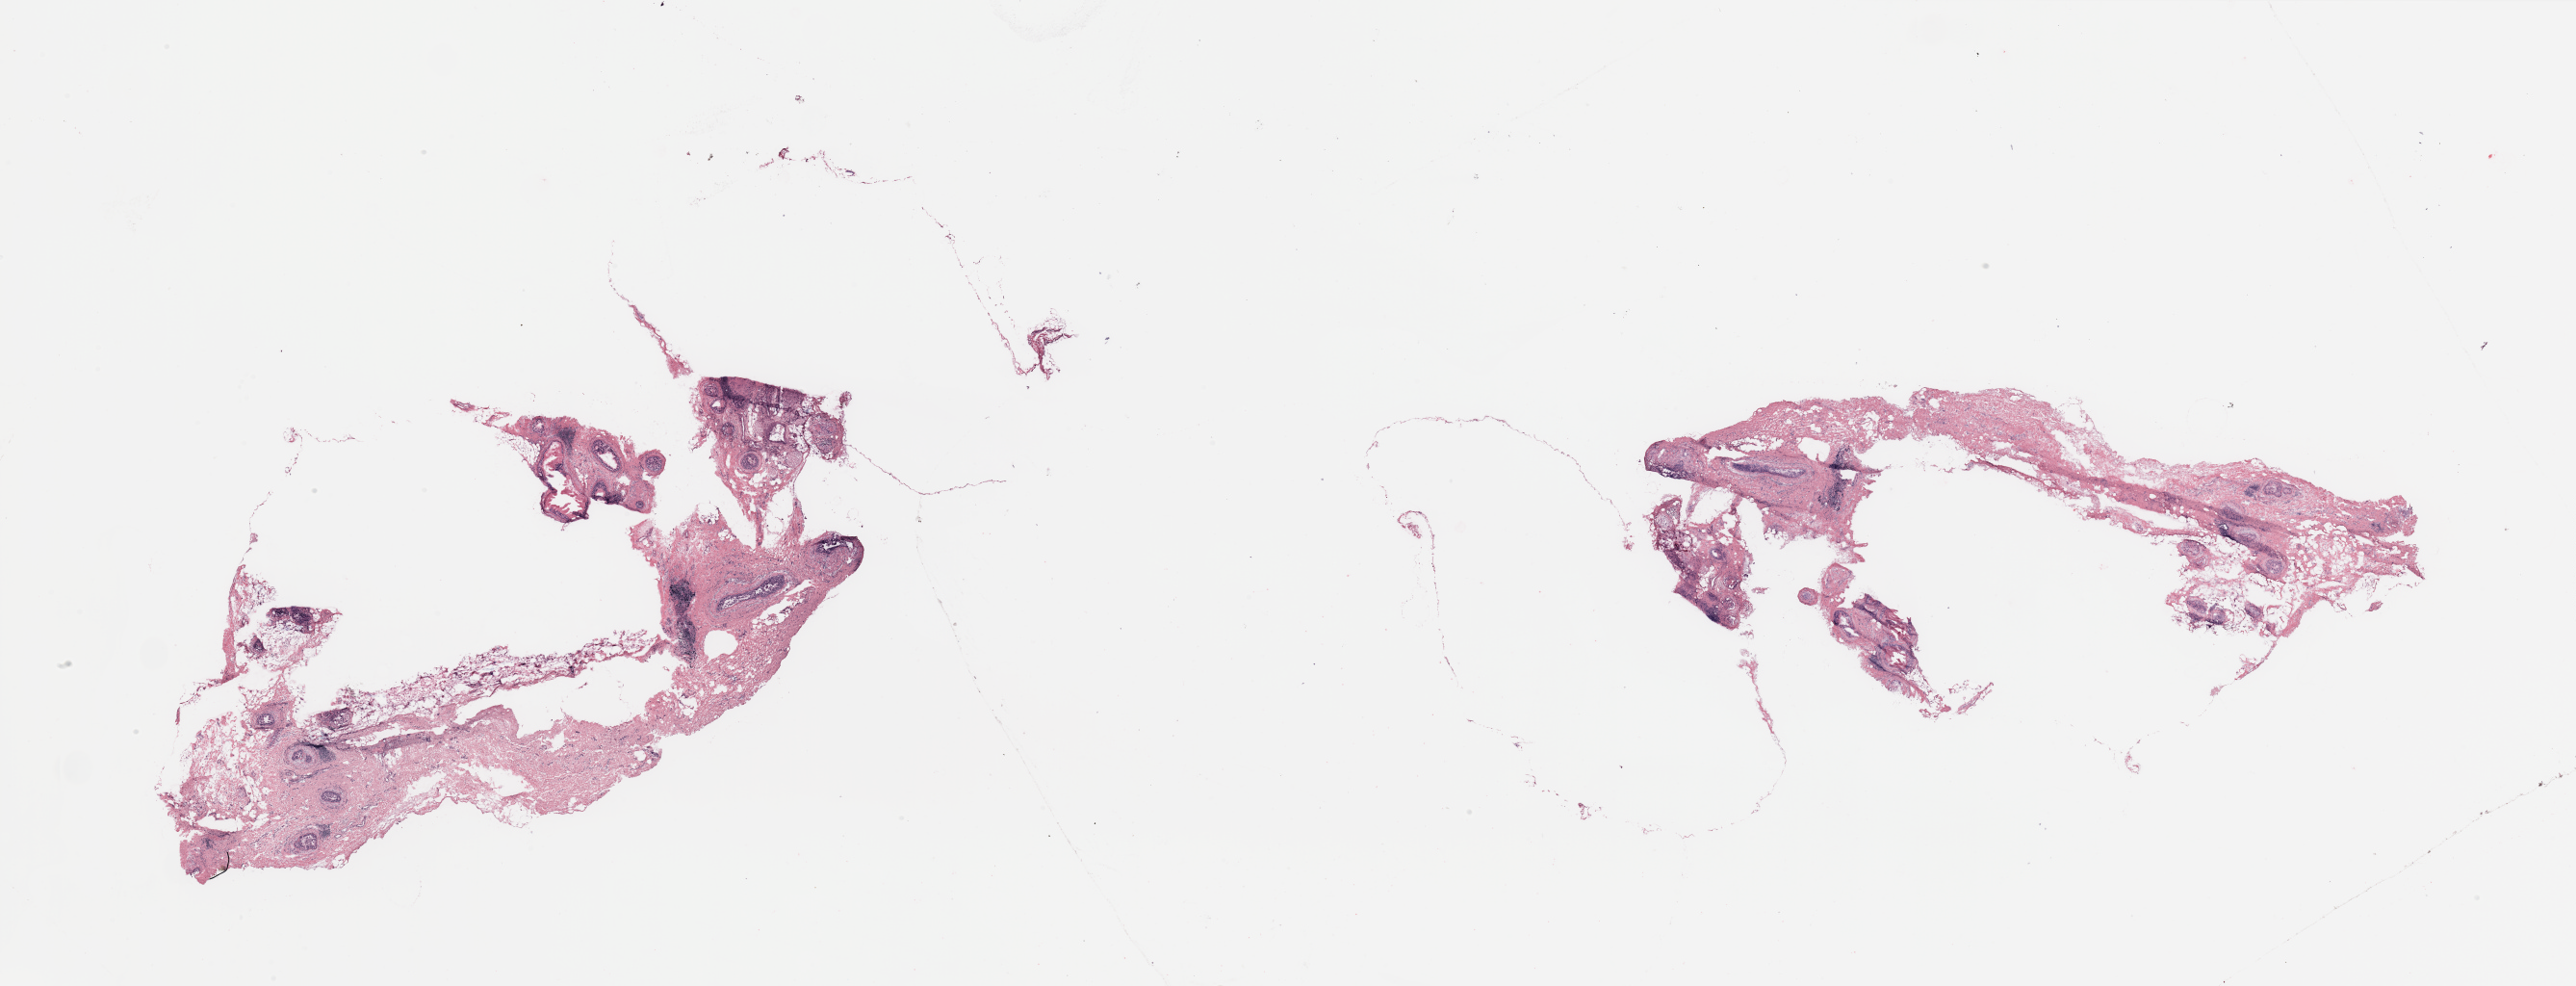
Digitized H&E-stained tissue section (whole slide), a low-resolution overview of the entire scanned area, about 42.3 x 16.2 mm (slide scanned at 20x), breast, tumour tissue. Patient: female, age 71 years.
Histologic diagnosis: Intraductal papillary carcinoma.